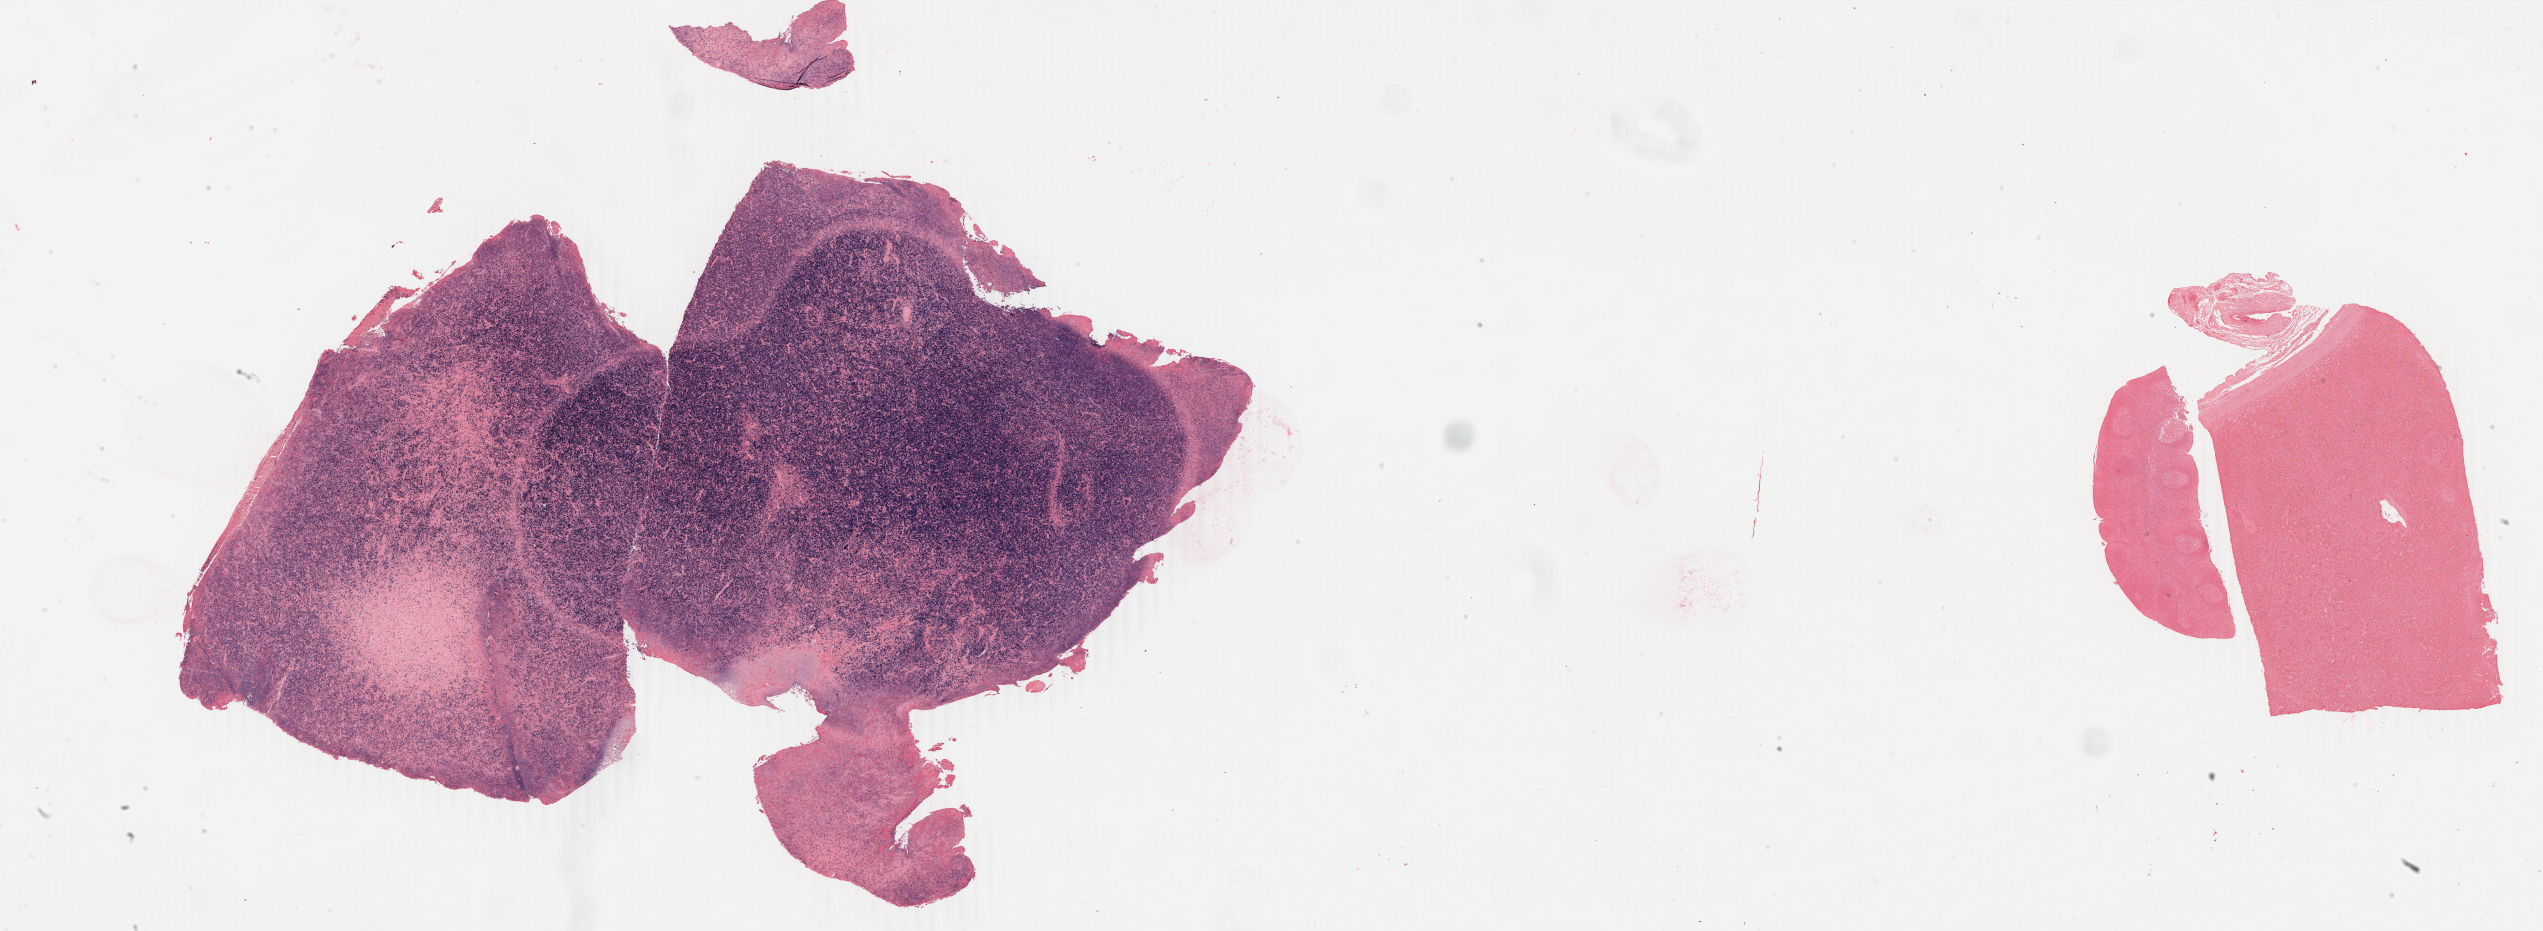
Whole-slide image, Epstein–Barr virus-encoded RNA (EBER) in-situ hybridisation, a low-resolution overview of the entire scanned area, about 40.5 x 14.8 mm. Specimen: tumor tissue. Patient: male, age at initial diagnosis 7 years.
- histologic diagnosis: Diffuse large B-cell lymphoma, NOS